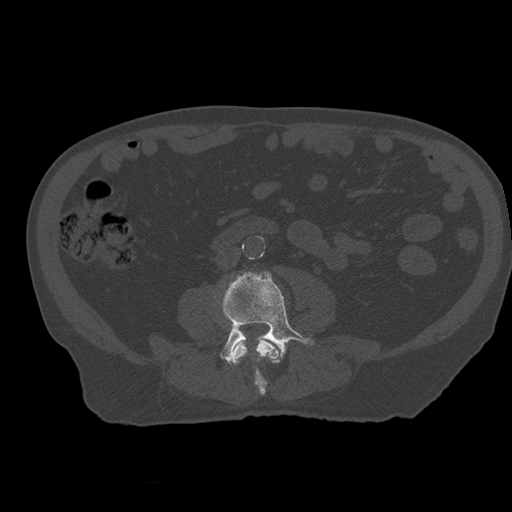
CT including the spine, one axial slice; slice 173 of 399 in the series (ordered by position); 120 kVp; bone window (W 1800 / L 400 HU); 1.25 mm slice thickness; 512 × 512 image matrix. Patient age 73 years. From the clinical record (not read from this slice): primary cancer: prostate.
Annotated regions visible in this slice (semi-automatic segmentation, software-assisted and operator-edited):
- L3 vertebra: bounding box (x1, y1, x2, y2) in pixels: (232, 338, 281, 396)
- L4 vertebra: (220, 271, 314, 365)